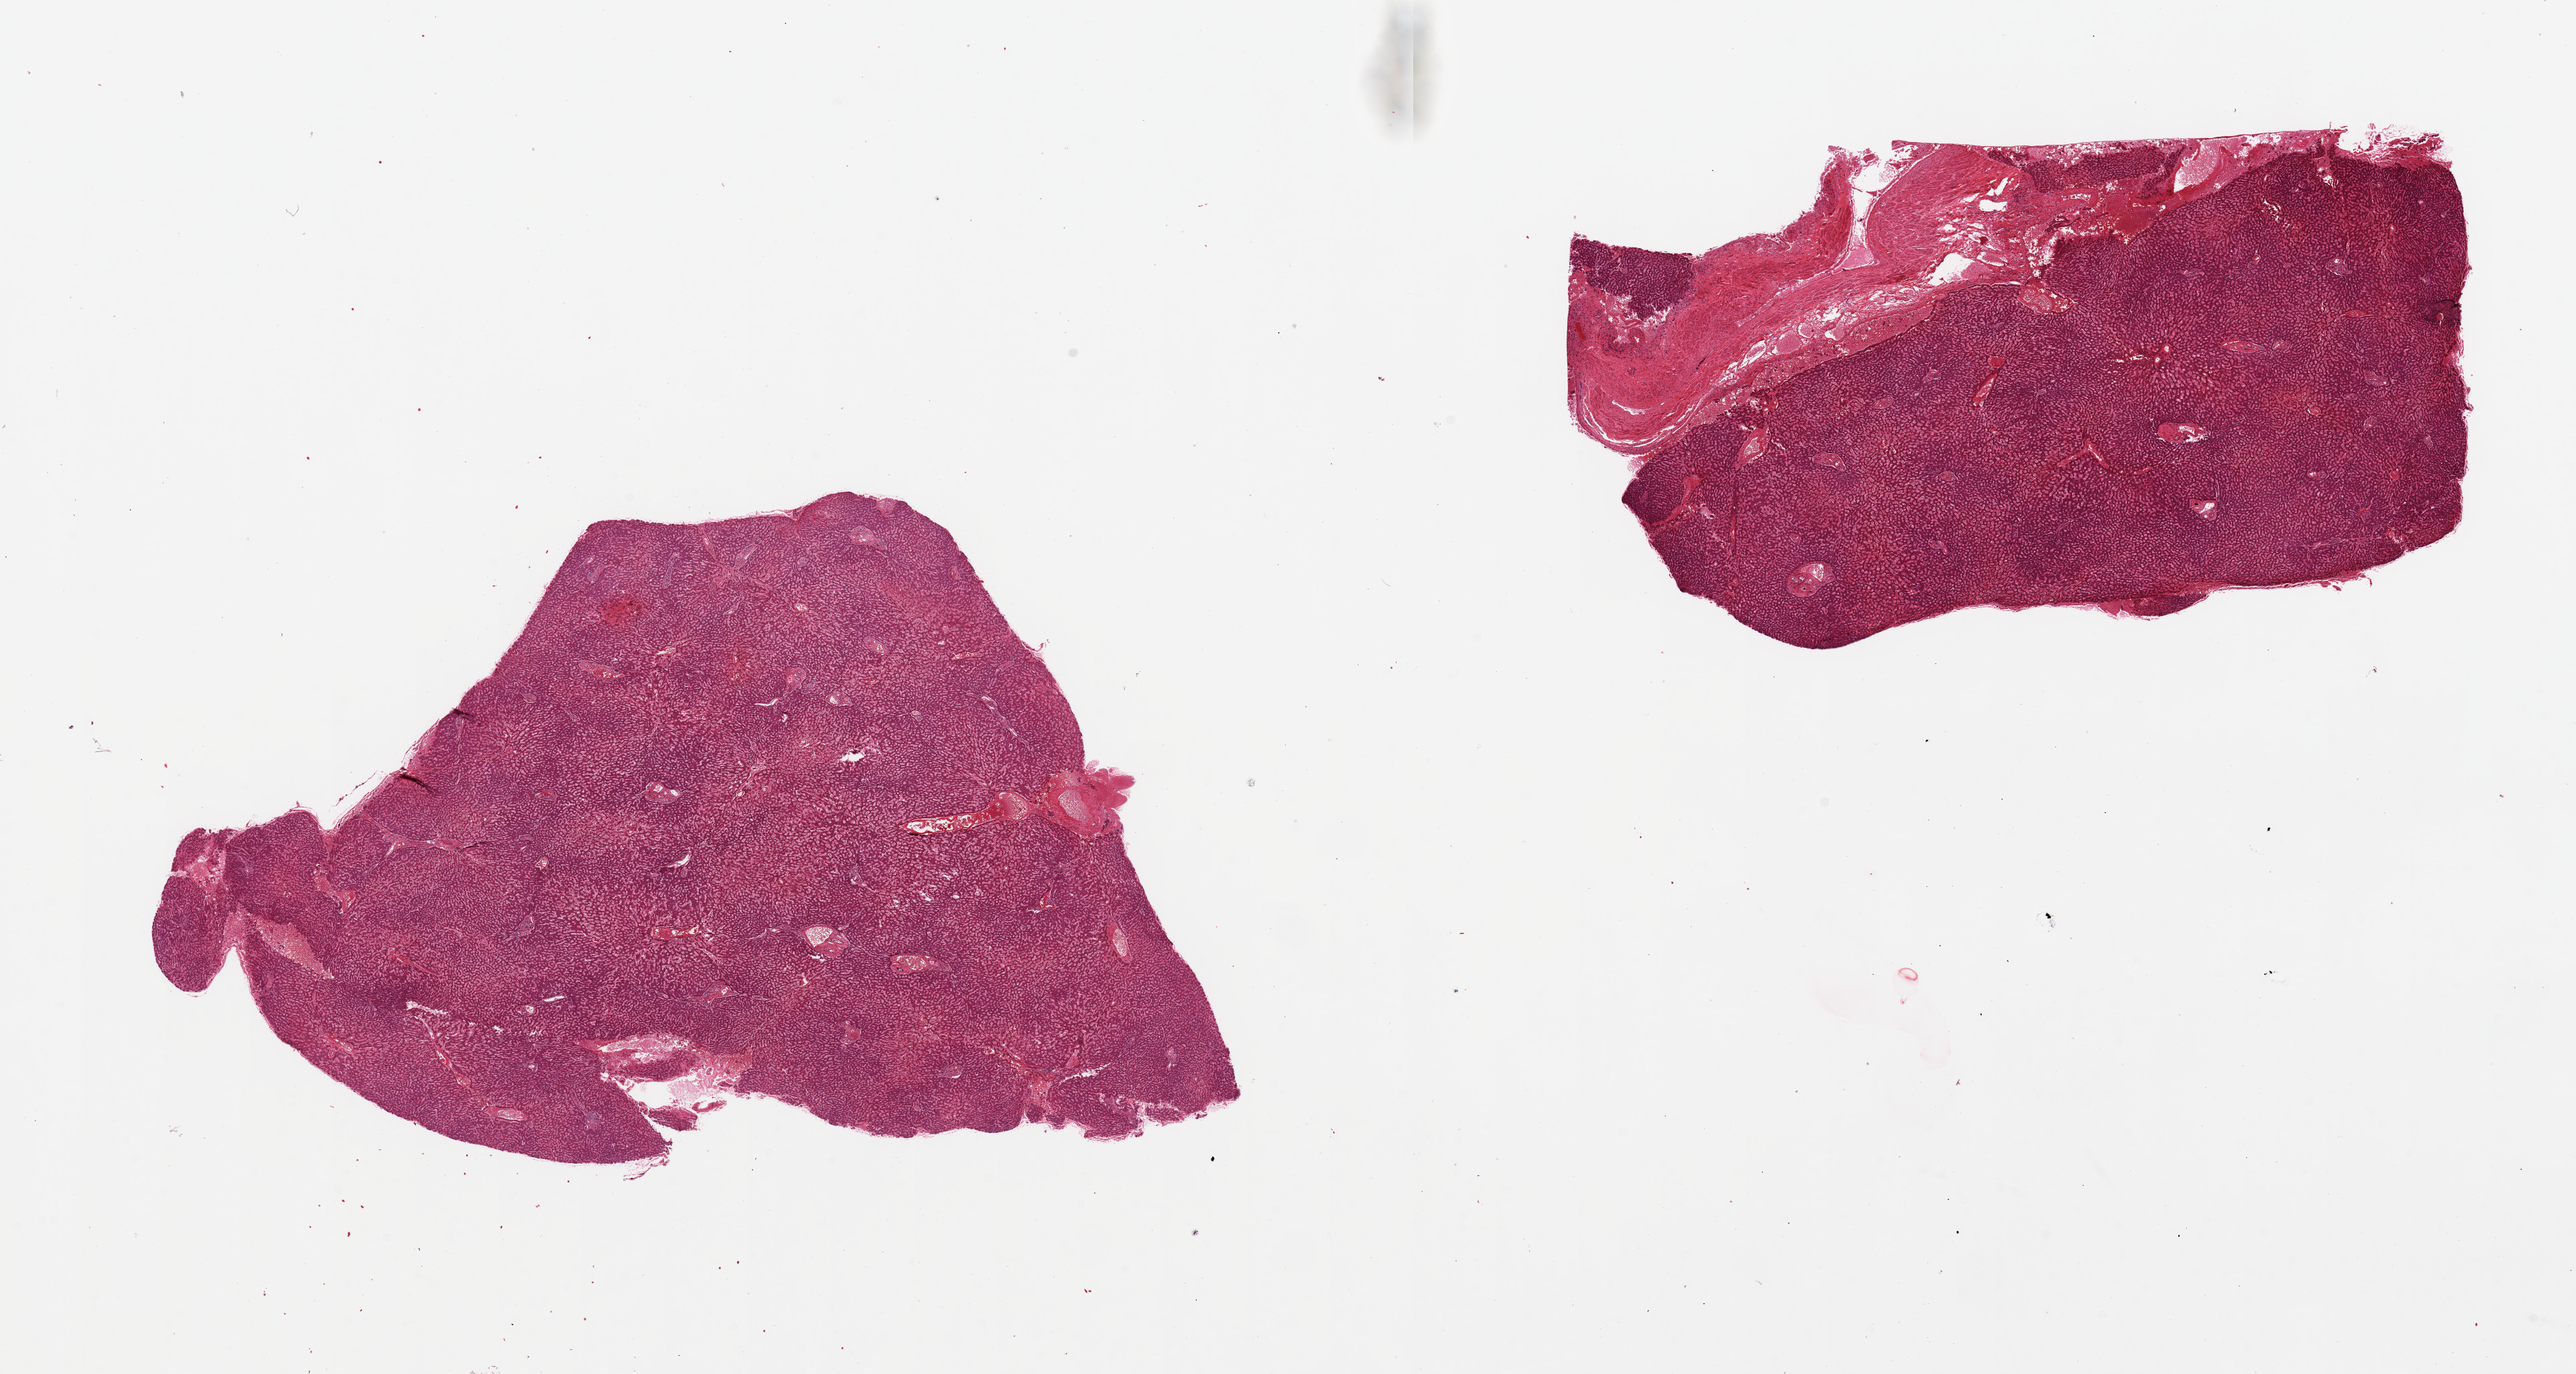
Whole-slide image, hematoxylin and eosin (H&E) stain — a low-resolution overview of the entire scanned area, about 30.5 x 16.3 mm (slide scanned at 20x), PAXgene-fixed, paraffin-embedded tissue, sampled site (target tissue): liver, tissue donor sample. Donor sex: female.
* reviewer comment on this tissue sample: 2 pieces, moderately autolyzed; no discernable steatosis, moderate-marked passive congestion